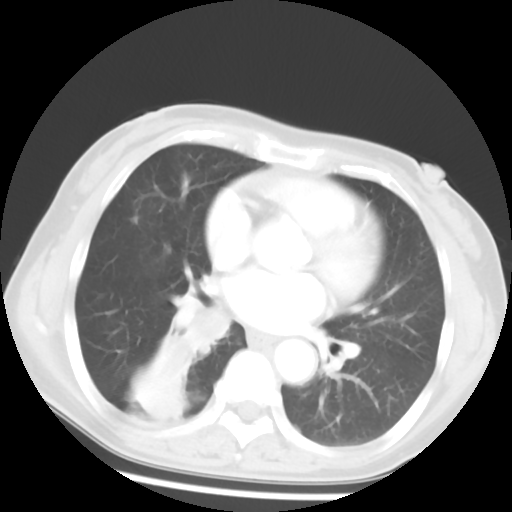
Chest CT, one axial slice; slice 26 of 52 in the series (ordered by position); reconstruction kernel STANDARD; 120 kVp; lung window (W 1500 / L -600 HU); 5 mm slice thickness; 512 × 512 image matrix, field of view 297 × 297 mm. Patient: female, 54 years. From the clinical record (not read from this slice): clinical TNM (as recorded): T1c N0 M0; histopathological grade: G1-2.
Annotated regions visible in this slice (rectangle marked by the reading radiologist):
- lung tumour (recorded histology: squamous cell carcinoma): bounding box <175,296,234,347> (left, top, right, bottom; pixels)